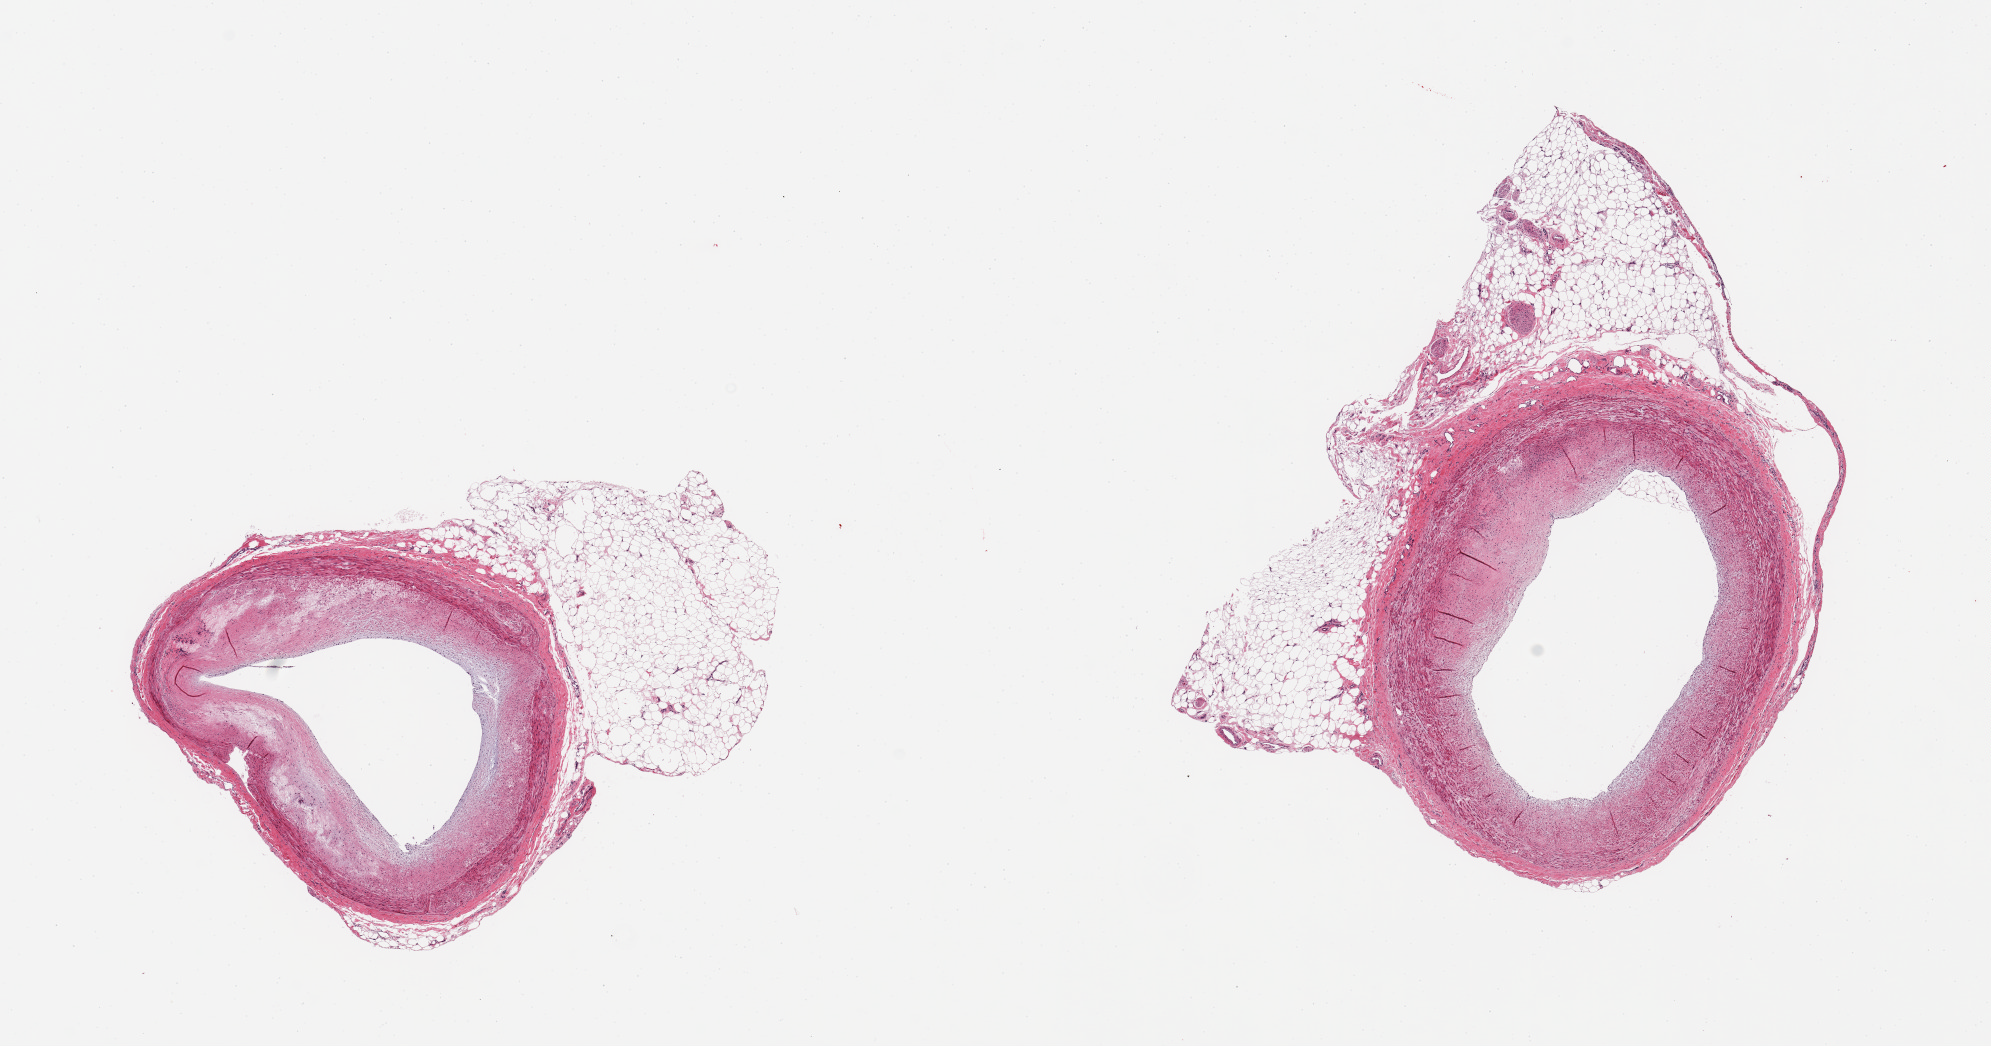
Digitized haematoxylin and eosin-stained section — low-resolution overview of the scanned area, about 15.8 x 8.3 mm (slide scanned at 20x). PAXgene-fixed, paraffin-embedded tissue. Sampled site (target tissue): coronary artery. Tissue donor sample. Donor: male.
Pathologist's review note for this sample: 2 pieces; atherosclerosis with narrowing of the lumen by ~25%, both include attached fat (1.7x2.8mm and 2.1x5.5mm).